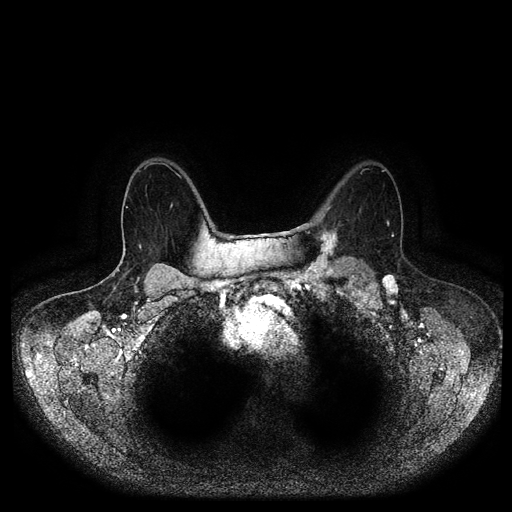
Breast MRI (dynamic contrast-enhanced, multi-phase), one axial slice; slice 68 of 116 in the series (ordered by position); dynamic contrast-enhanced series, time point 2 of 5 at this slice position (early post-contrast); 1.5 T; TE 2.6 ms, TR 5.2 ms; 2 mm slice thickness; 512 × 512 image matrix, field of view 380 × 380 mm. Patient: female, 69 years.
Outlined on this slice (semi-automatic segmentation, software-assisted and operator-edited):
- breast lesion (labelled 'tumour' in the annotation; benign lesions carry a separate 'benign' label): bounding box (x1, y1, x2, y2) in pixels: (303, 223, 342, 277)